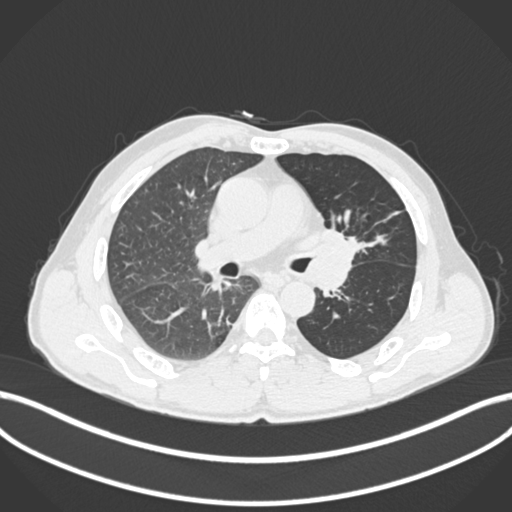
Chest CT, one axial slice; reconstruction kernel B30f; 120 kVp; lung window (W 1500 / L -600 HU); 512 × 512 image matrix, field of view 400 × 400 mm. Patient: male, 57 years. From the clinical record (not read from this slice): clinical TNM (as recorded): T2b N0 M0.
Structures marked on this image (rectangle marked by the reading radiologist):
- lung tumour (recorded histology: squamous cell carcinoma): bounding box [x1, y1, x2, y2] px = [312, 226, 373, 264]